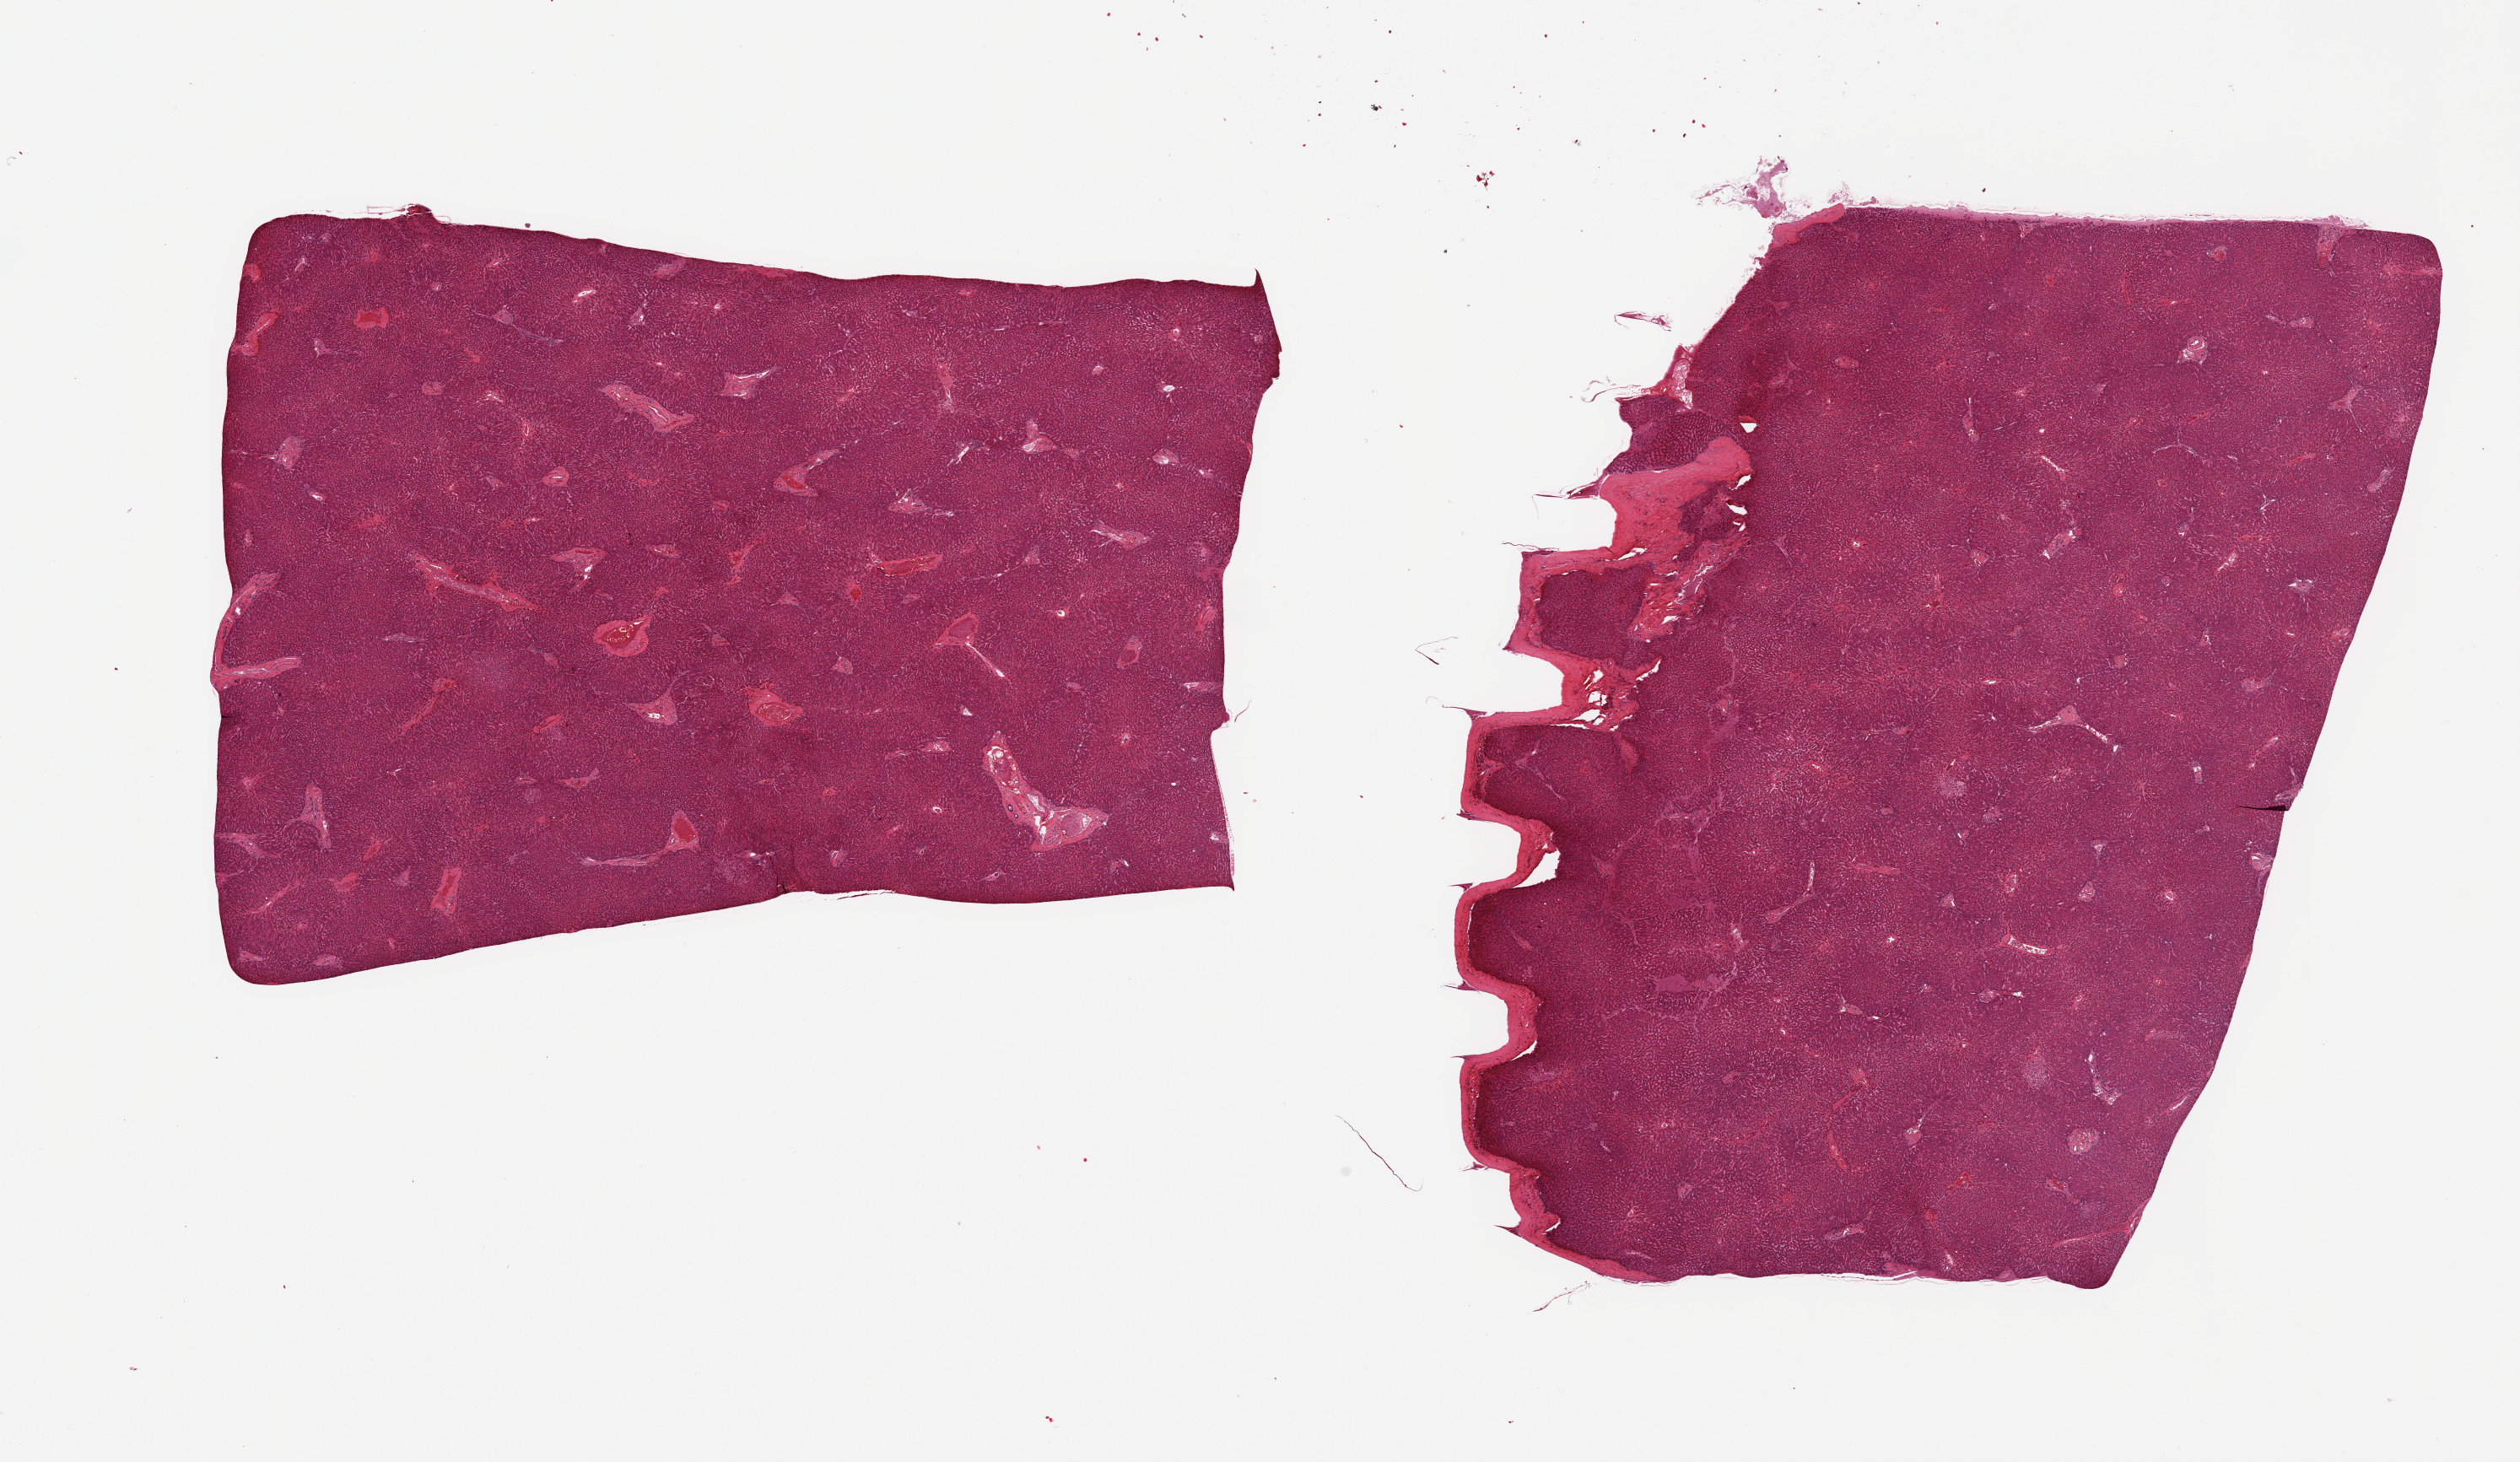
Whole-slide image, haematoxylin and eosin stain, whole scanned area (about 23.6 x 13.7 mm, from a 20x scan) shown as a low-resolution overview, PAXgene-fixed paraffin-embedded (PFPE) section, section of liver (target tissue), donor tissue sample. Donor: male.
Pathologist's review note for this sample: 2 pieces, no steatosis.